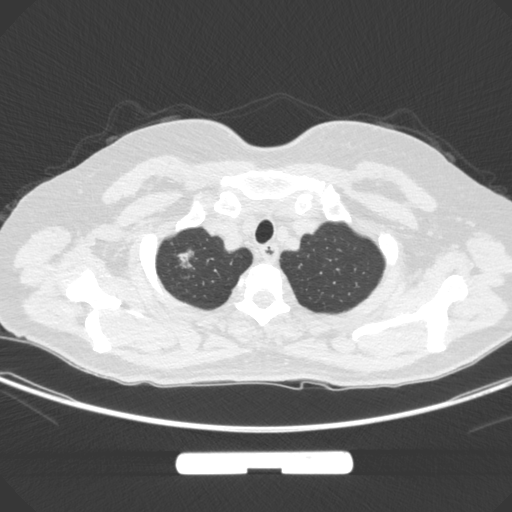
Chest CT, one axial slice; slice 262 of 295 in the series (ordered by position); lung window (W 1500 / L -600 HU); 1 mm slice thickness; 512 × 512 image matrix, field of view 369 × 369 mm. Patient: female, 58 years. From the clinical record (not read from this slice): clinical TNM (as recorded): T1b N0 M0; histopathological grade: G2-3.
Annotated regions visible in this slice (bounding box drawn by a radiologist):
- lung tumour (recorded histology: adenocarcinoma): box from (x=168, y=240) to (x=198, y=277) px